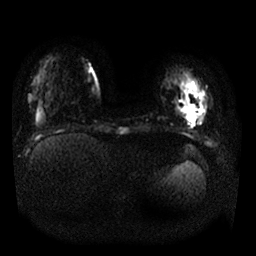
Breast MRI, one axial slice. Slice 5 of 25 in the series (ordered by position). Diffusion-weighted series; image 2 of 4 stored at this slice position (different b-values; order by instance number). 1.5 T. 4 mm slice thickness. 256 × 256 image matrix. Female patient.
Structures marked on this image (manually delineated by an expert):
- tumour on diffusion-weighted imaging: bounding box (x1, y1, x2, y2) in pixels: (182, 95, 198, 119)